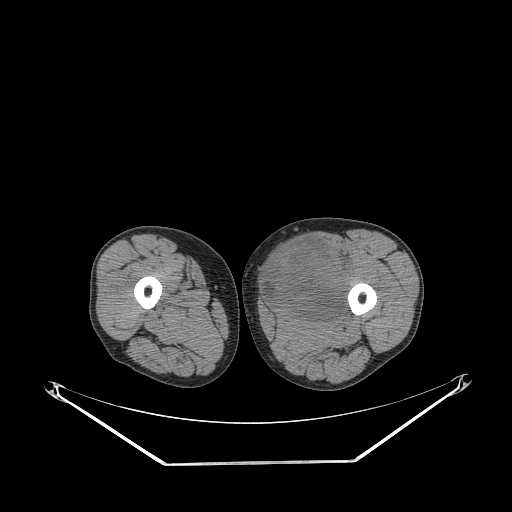
CT of an extremity soft-tissue mass (from a PET/CT study), one axial slice; slice 240 of 267 in the series (ordered by position); 140 kVp; soft-tissue window (W 400 / L 40 HU); 512 × 512 image matrix, field of view 500 × 500 mm. Male patient. Case-level facts recorded for this patient, not image findings: histological type: pleiomorphic liposarcoma; grade: high; site of the primary tumour: left thigh.
Annotated regions visible in this slice (expert contour drawn on MRI and transferred to this co-registered scan by the dataset authors):
- gross tumour volume including surrounding oedema: bounding box [x1, y1, x2, y2] px = [265, 237, 355, 321]
- gross tumour volume (mass): [265, 237, 350, 321]